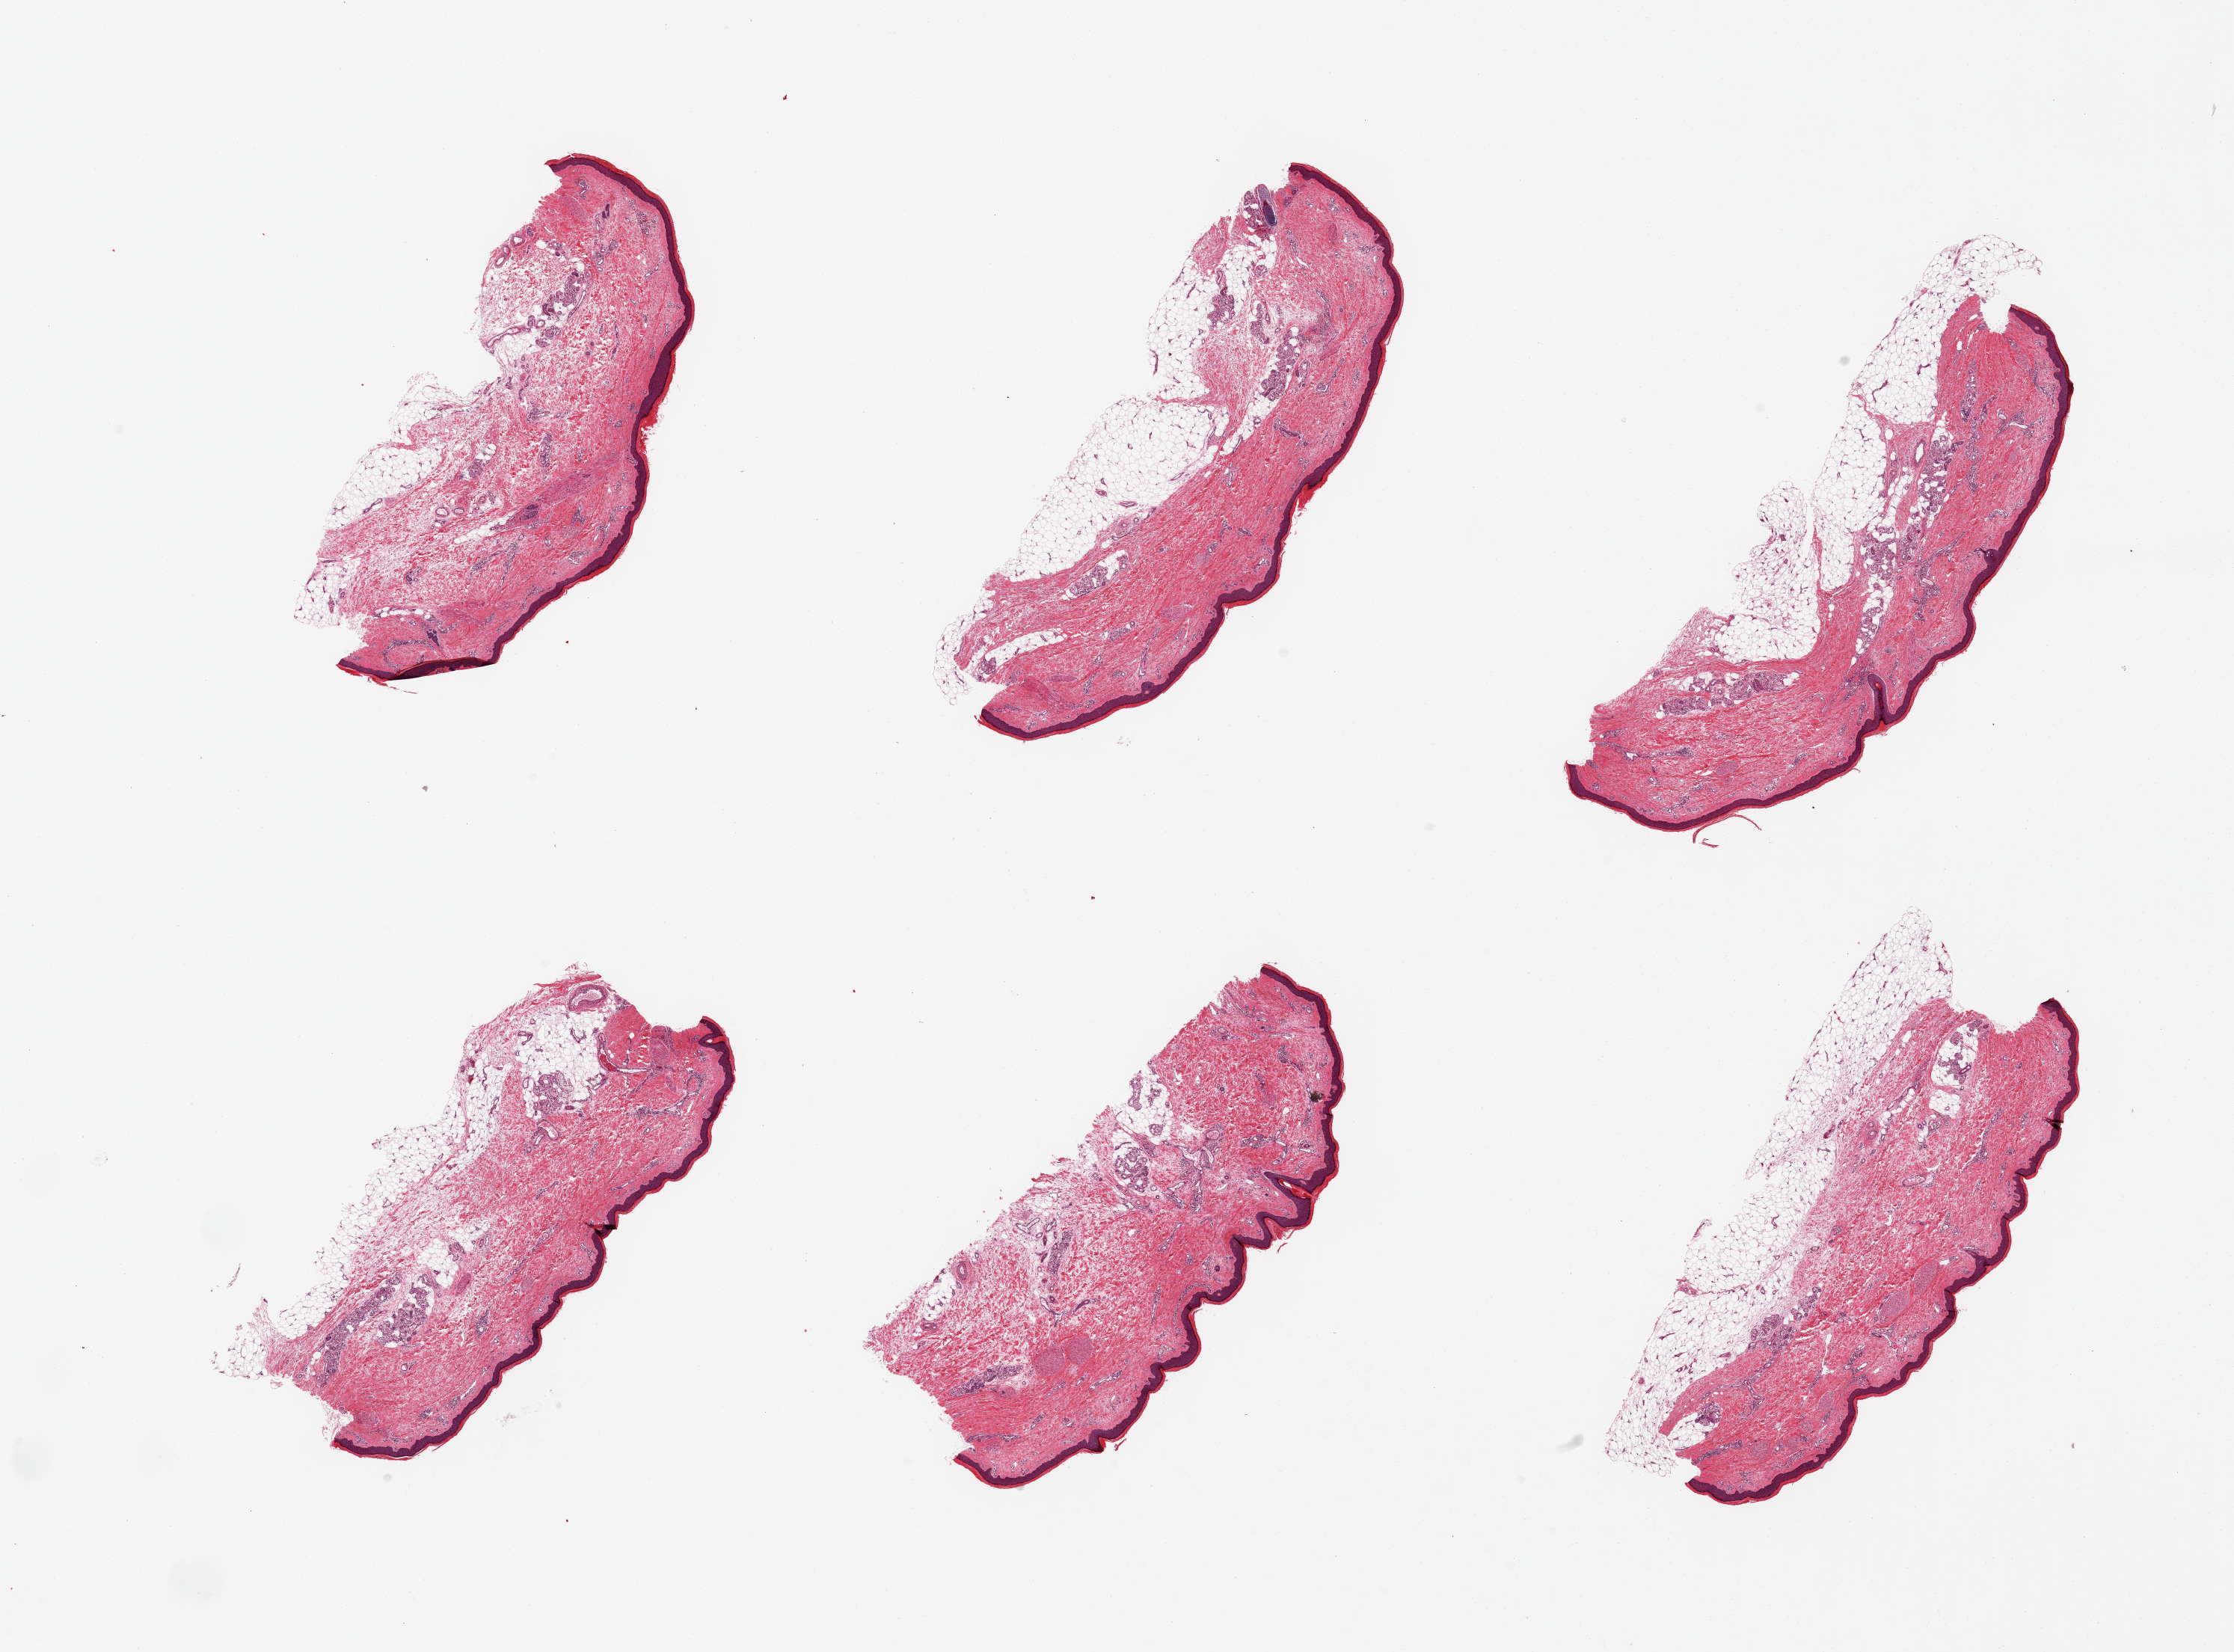
Digitized H&E-stained section — a low-resolution overview of the entire scanned area, about 23.6 x 17.5 mm (slide scanned at 20x). PAXgene-fixed, paraffin-embedded tissue. Target tissue: skin of lower leg. Donor tissue sample. Donor sex: male.
Pathologist's review note for this sample: 6 pieces; 5 of 6 have subcutaneous fat, up to 0.8mm thick; 10% dermal fat.